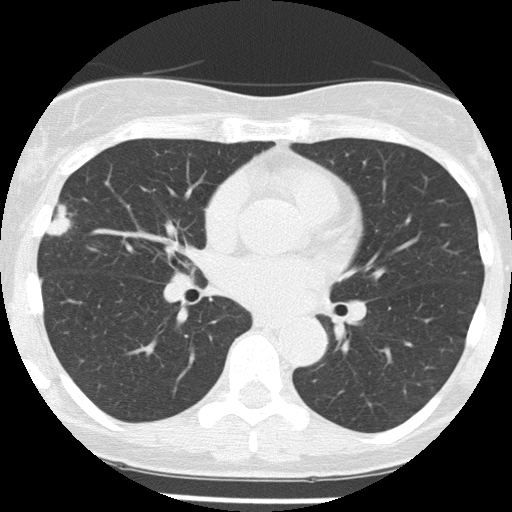
Chest CT (low-dose screening protocol), one axial image; baseline screening round; lung window (W 1500 / L -600 HU); 2 mm slice thickness; slice 74 of 156 in the series. Female, age 58 years at enrolment. Former smoker at enrolment.
Expert reader's lesion annotation, bounding box <29,195,86,254> (left, top, right, bottom; pixels). Reader record for this screening exam (exam-level; its link to the box is not recorded): non-calcified nodule or mass ≥4 mm, right middle lobe, 18 × 9 mm, spiculated (stellate) margins, soft tissue attenuation.